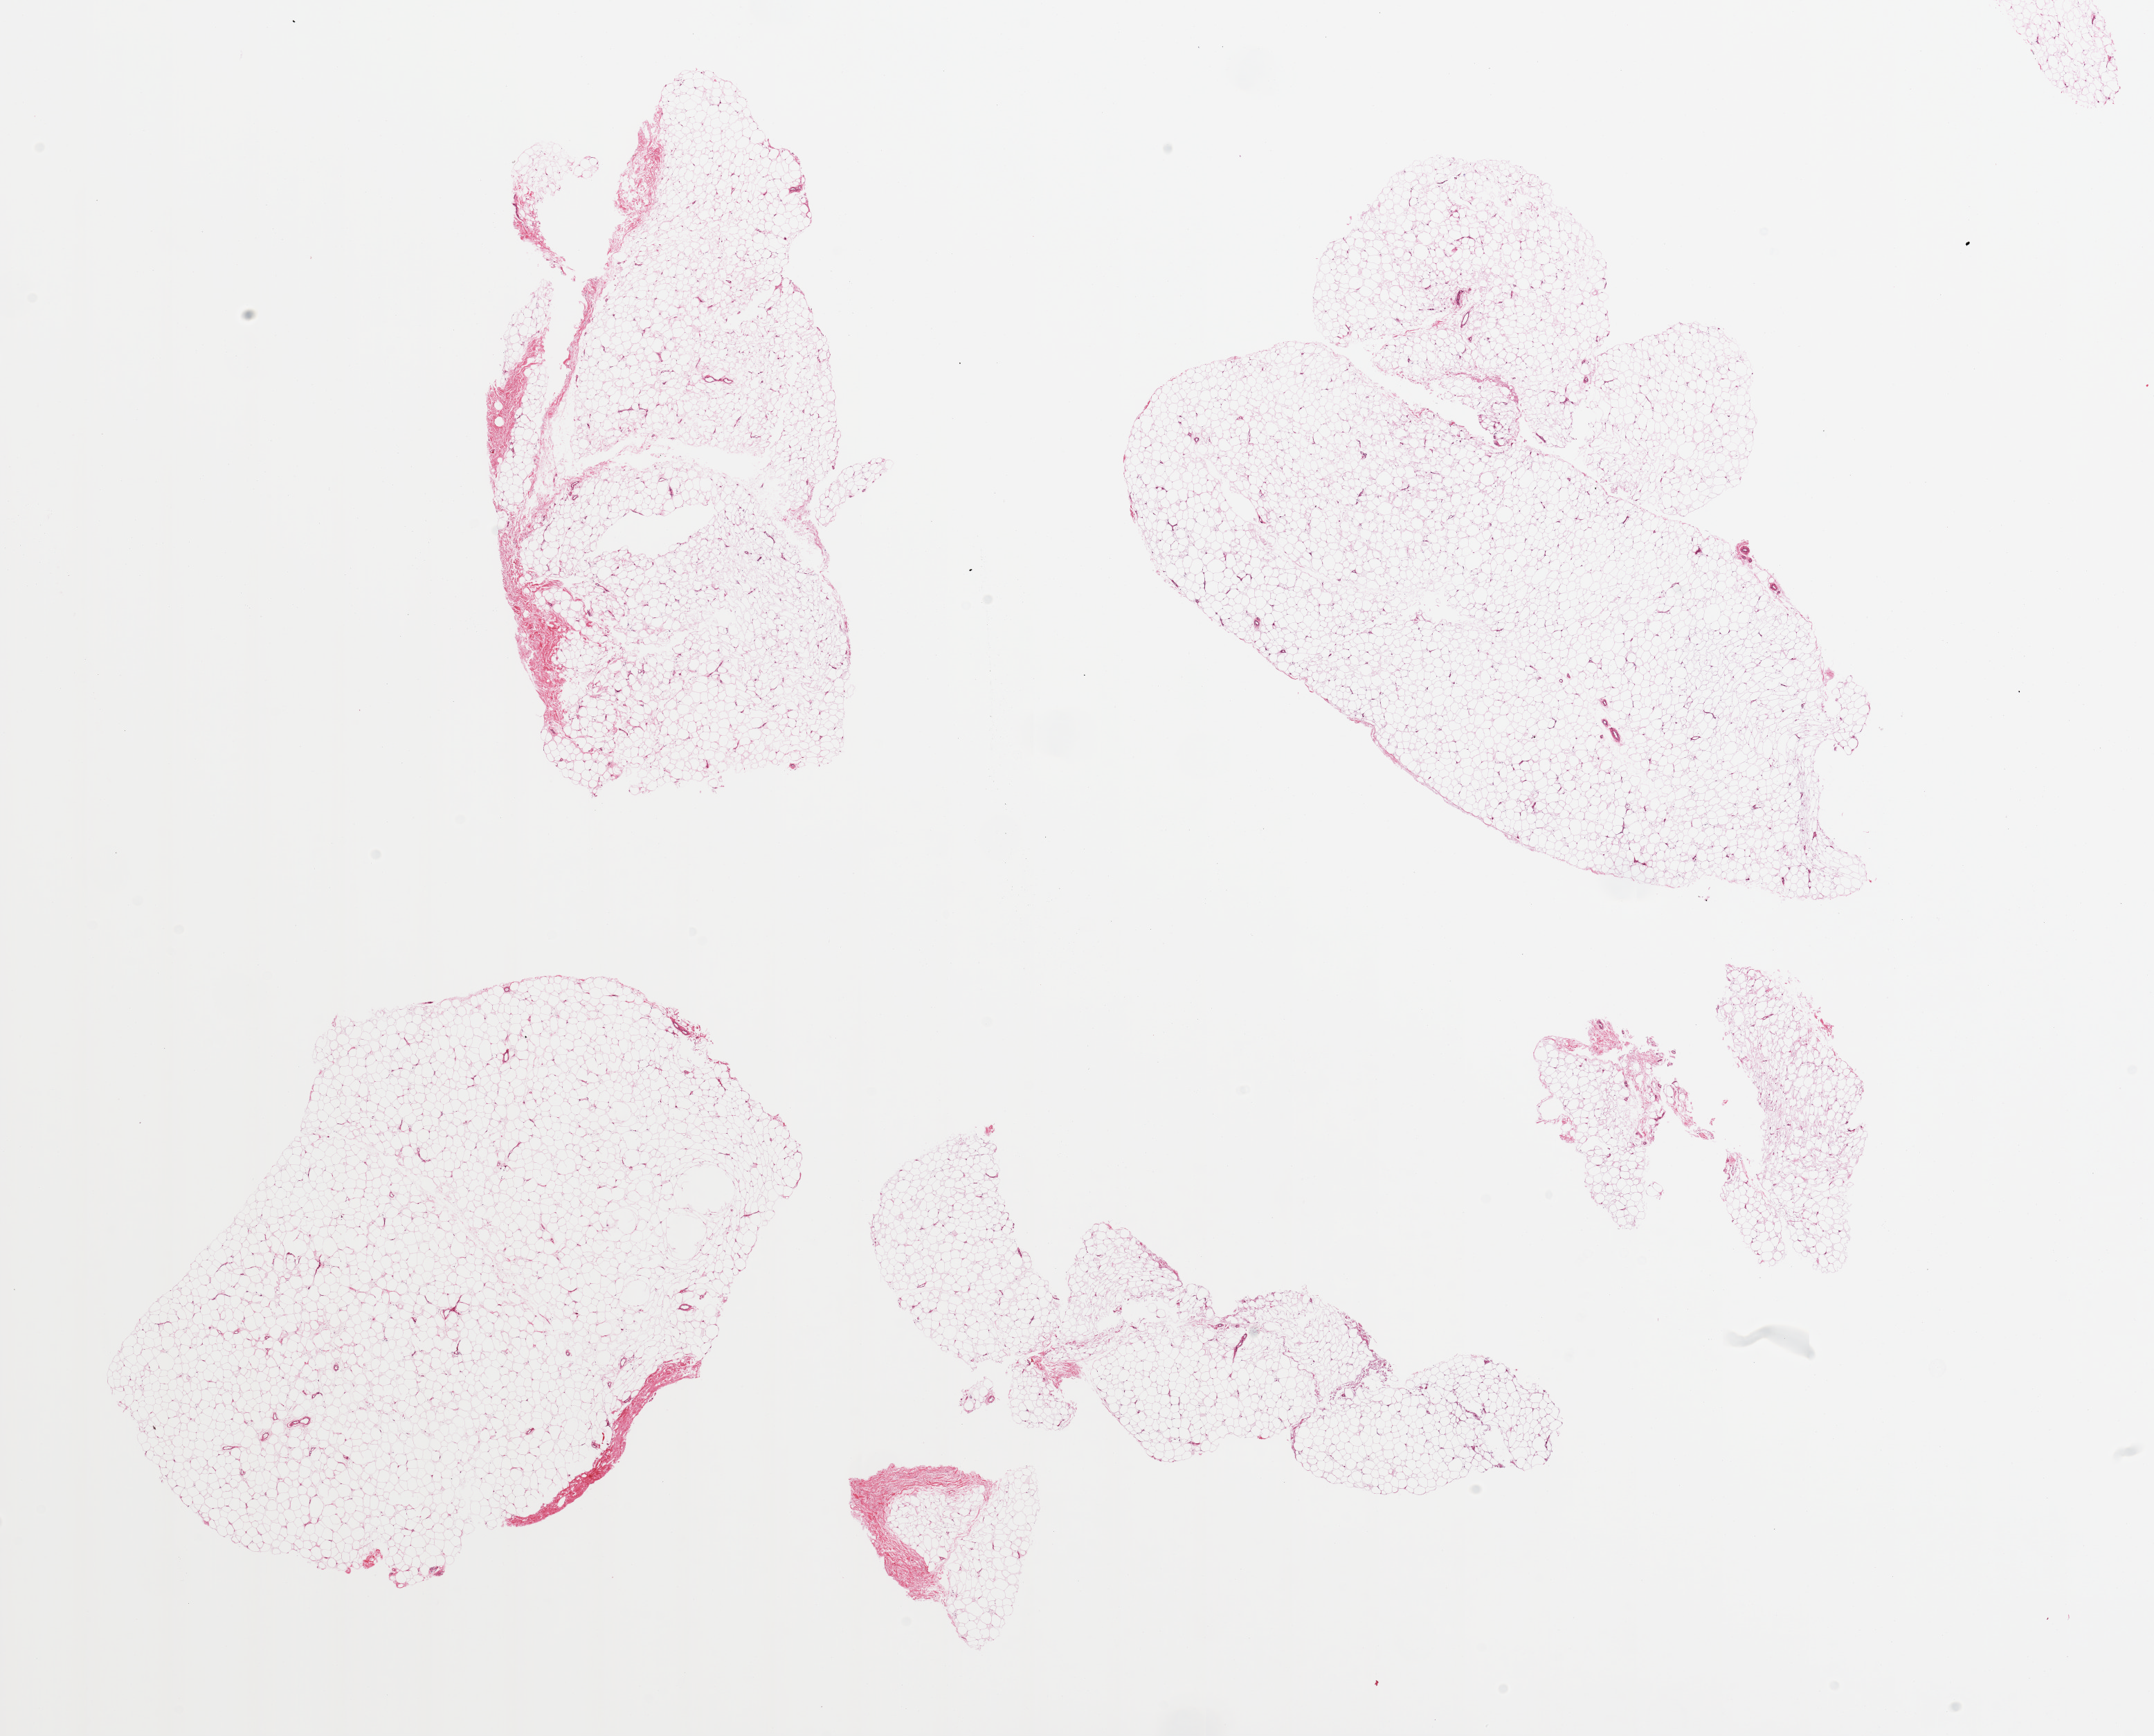
Haematoxylin and eosin whole-slide image — shown as a low-resolution overview of the whole scanned area (about 24.6 x 19.8 mm). PAXgene-fixed, paraffin-embedded tissue. Sampled site (target tissue): adipose tissue. Tissue donor sample. Male donor.
Pathologist's review note for this sample: 4 pieces.